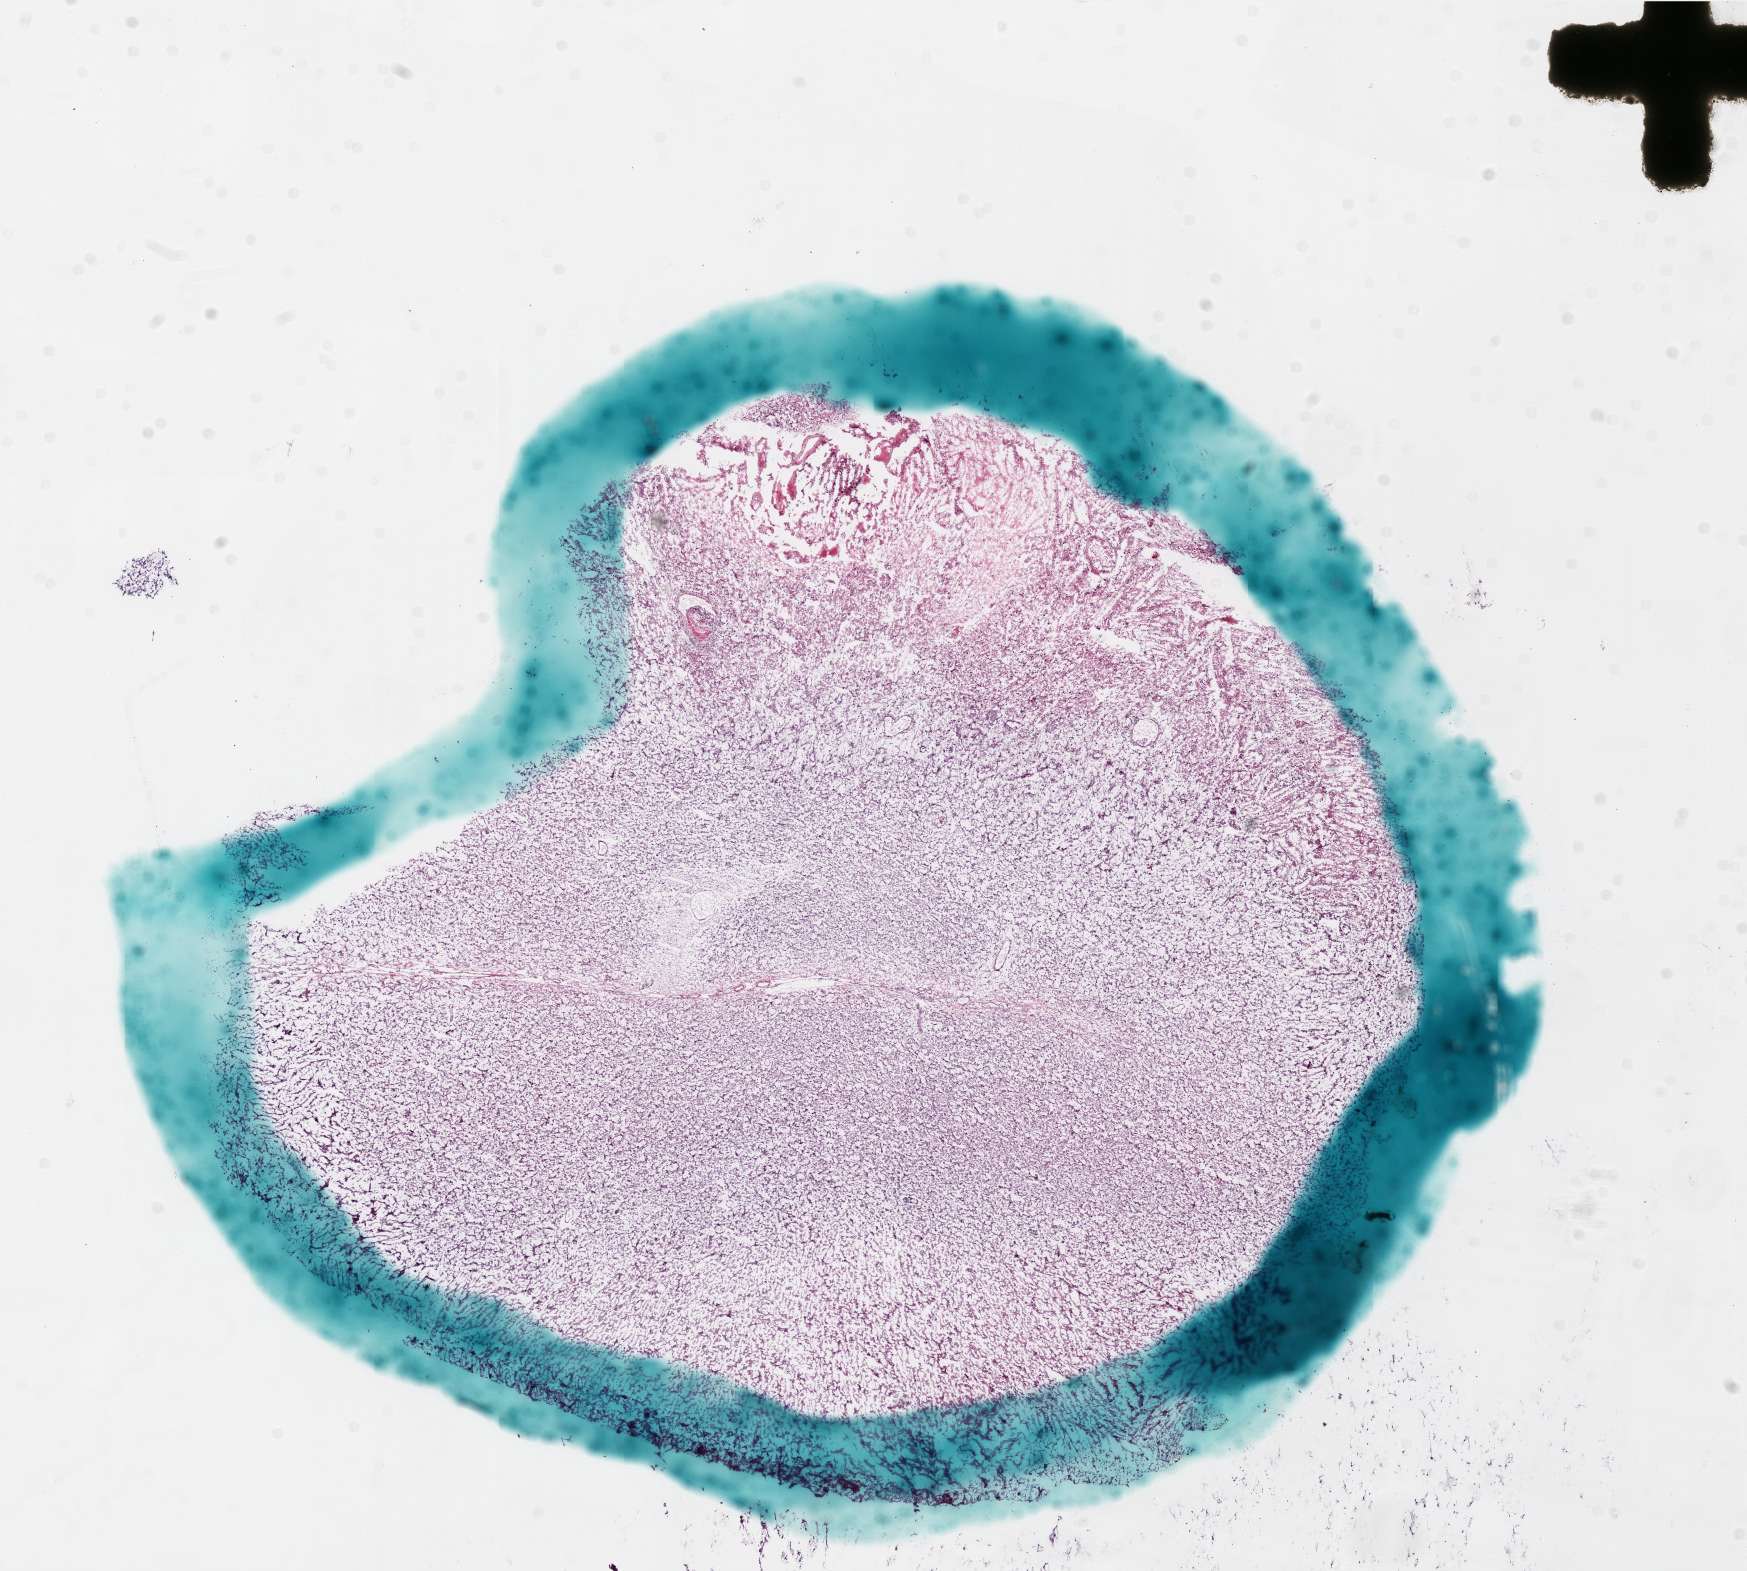
Digitized Hematoxylin and eosin (H&E) stained tissue section (whole slide), low-resolution overview of the scanned area, about 14.0 x 12.6 mm (acquisition: 20x scan), frozen section from the bottom of the tissue portion, primary tumour sample from the brain. Male, age 45 years at initial diagnosis. Composition of this section per pathologist review: tumour cells 0%, tumour nuclei 75%, normal cells 0%, stromal cells 80%, necrosis 20%.
Pathologic diagnosis: Glioblastoma.